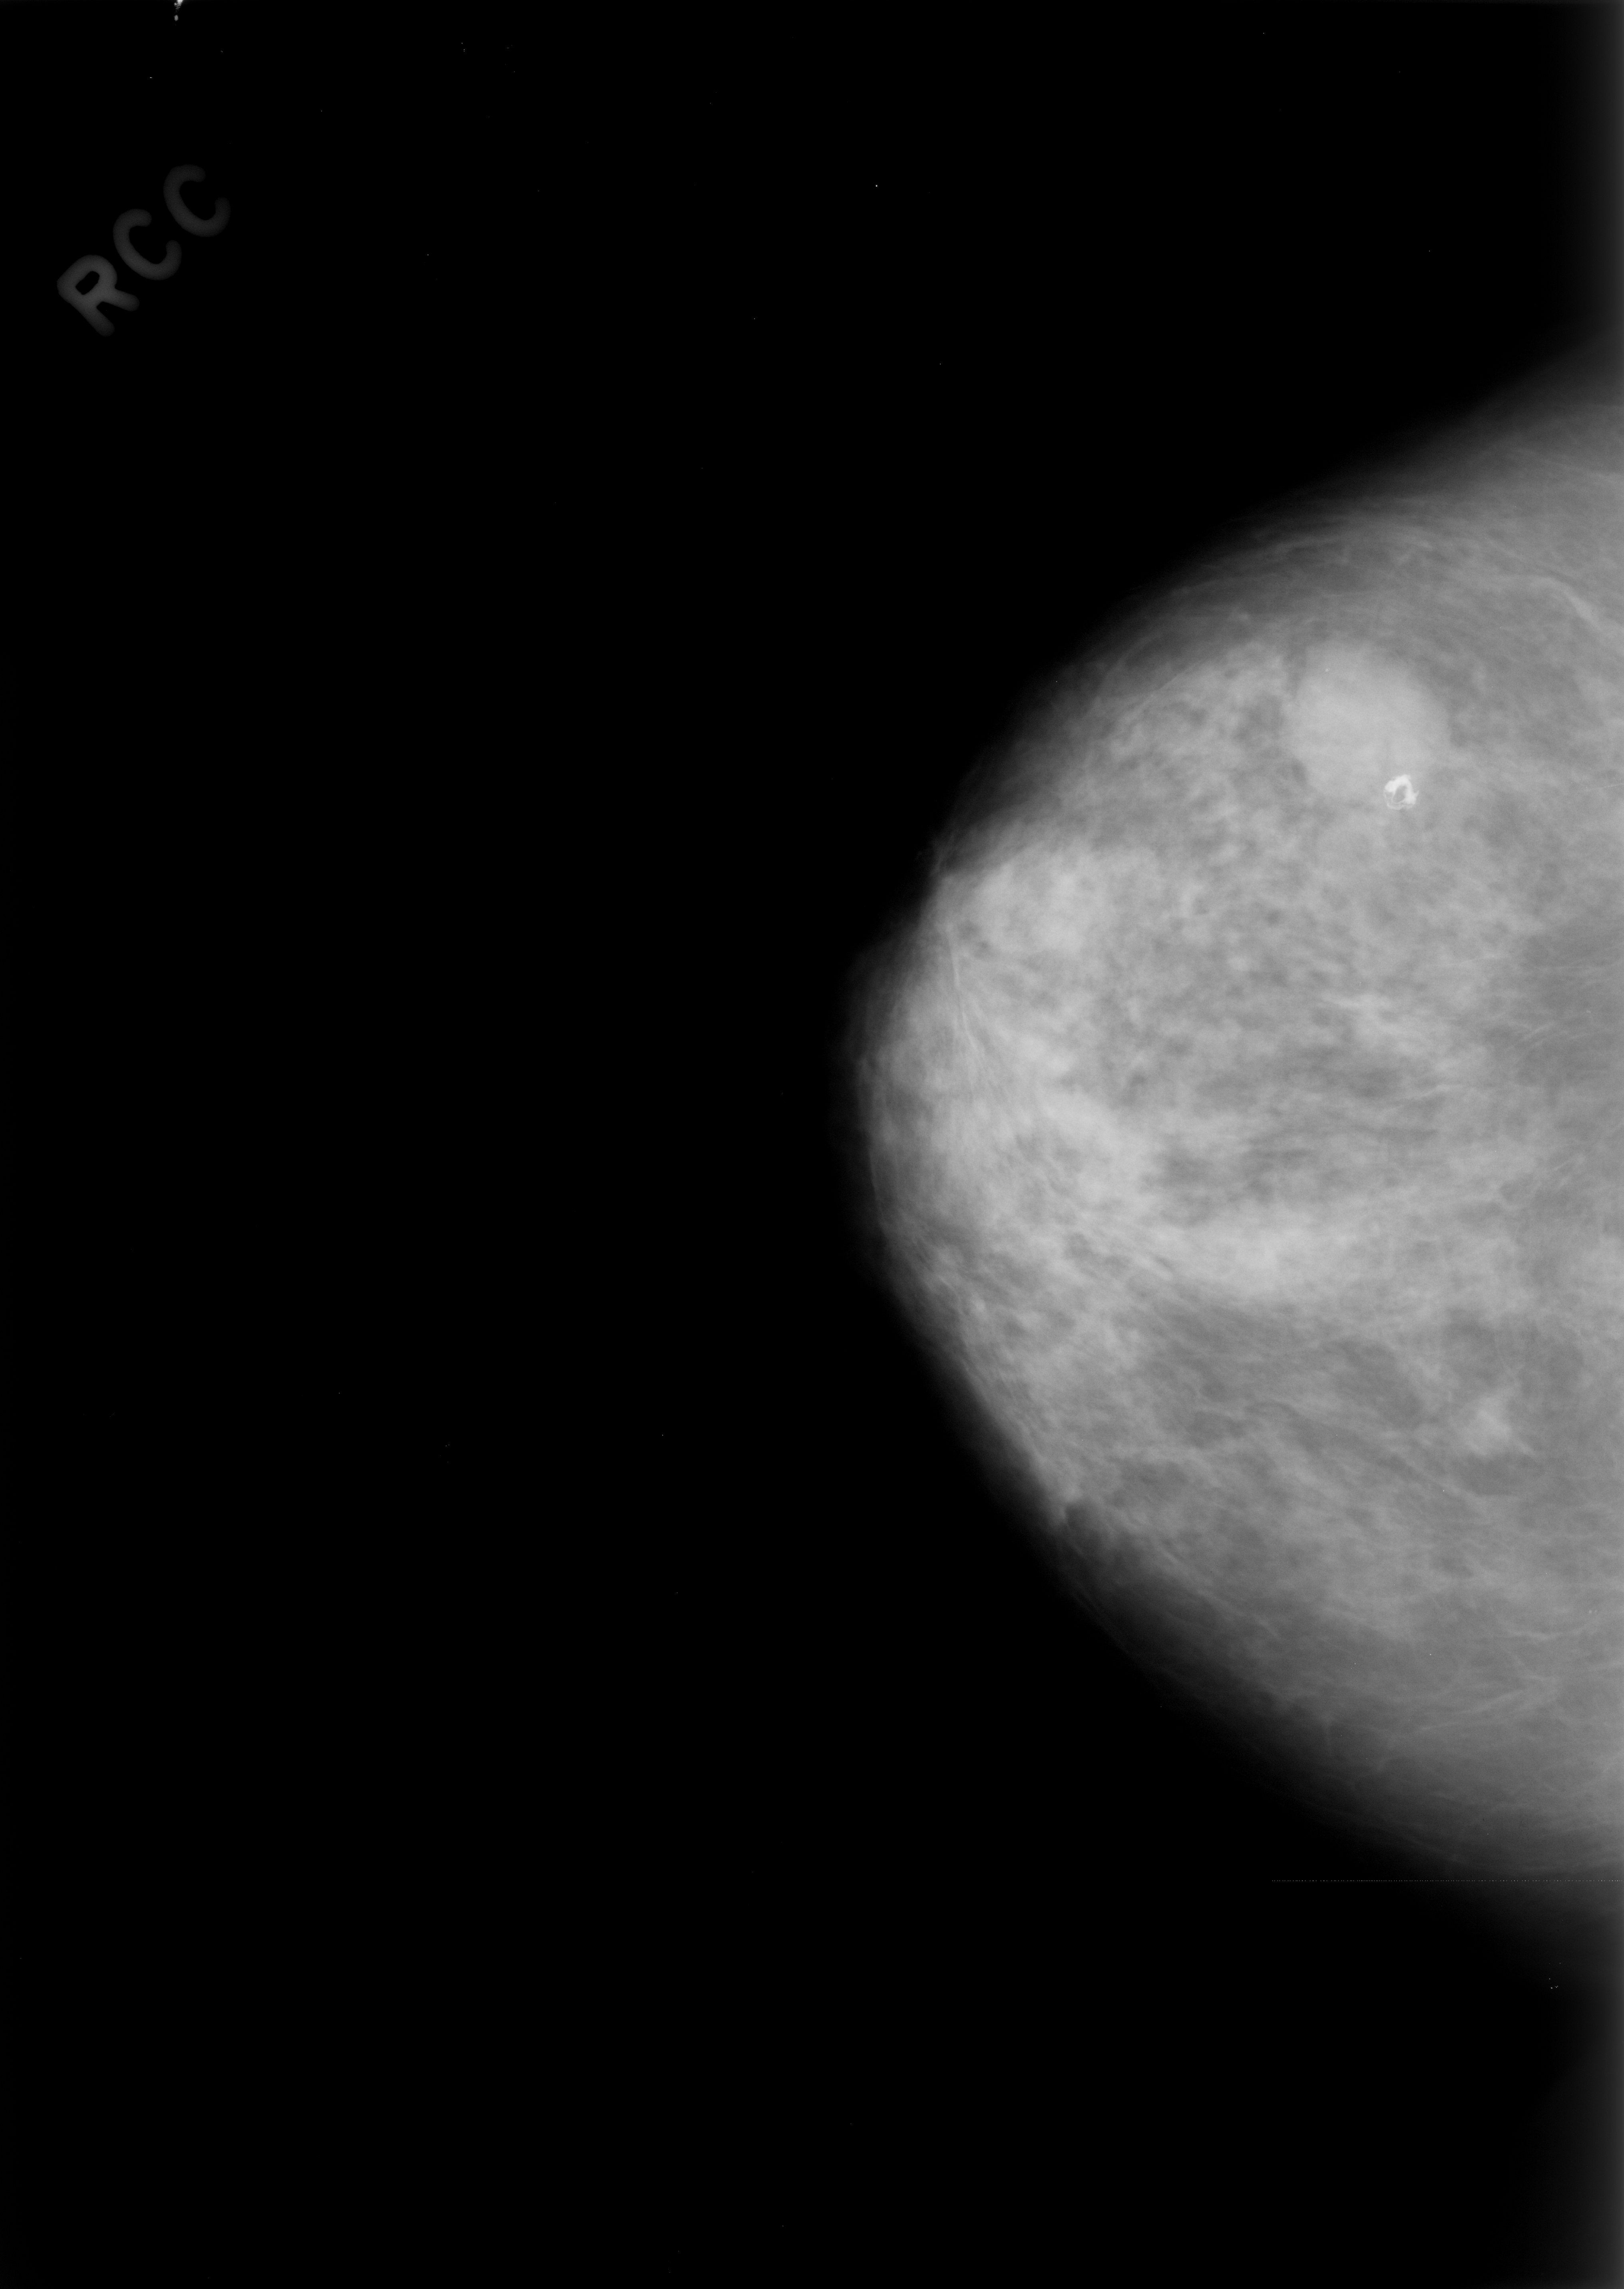
Digitized screen-film mammogram, right breast, craniocaudal (CC) view.
Mass, shape round, margins microlobulated; BI-RADS assessment category 4; pathology (as recorded): benign.